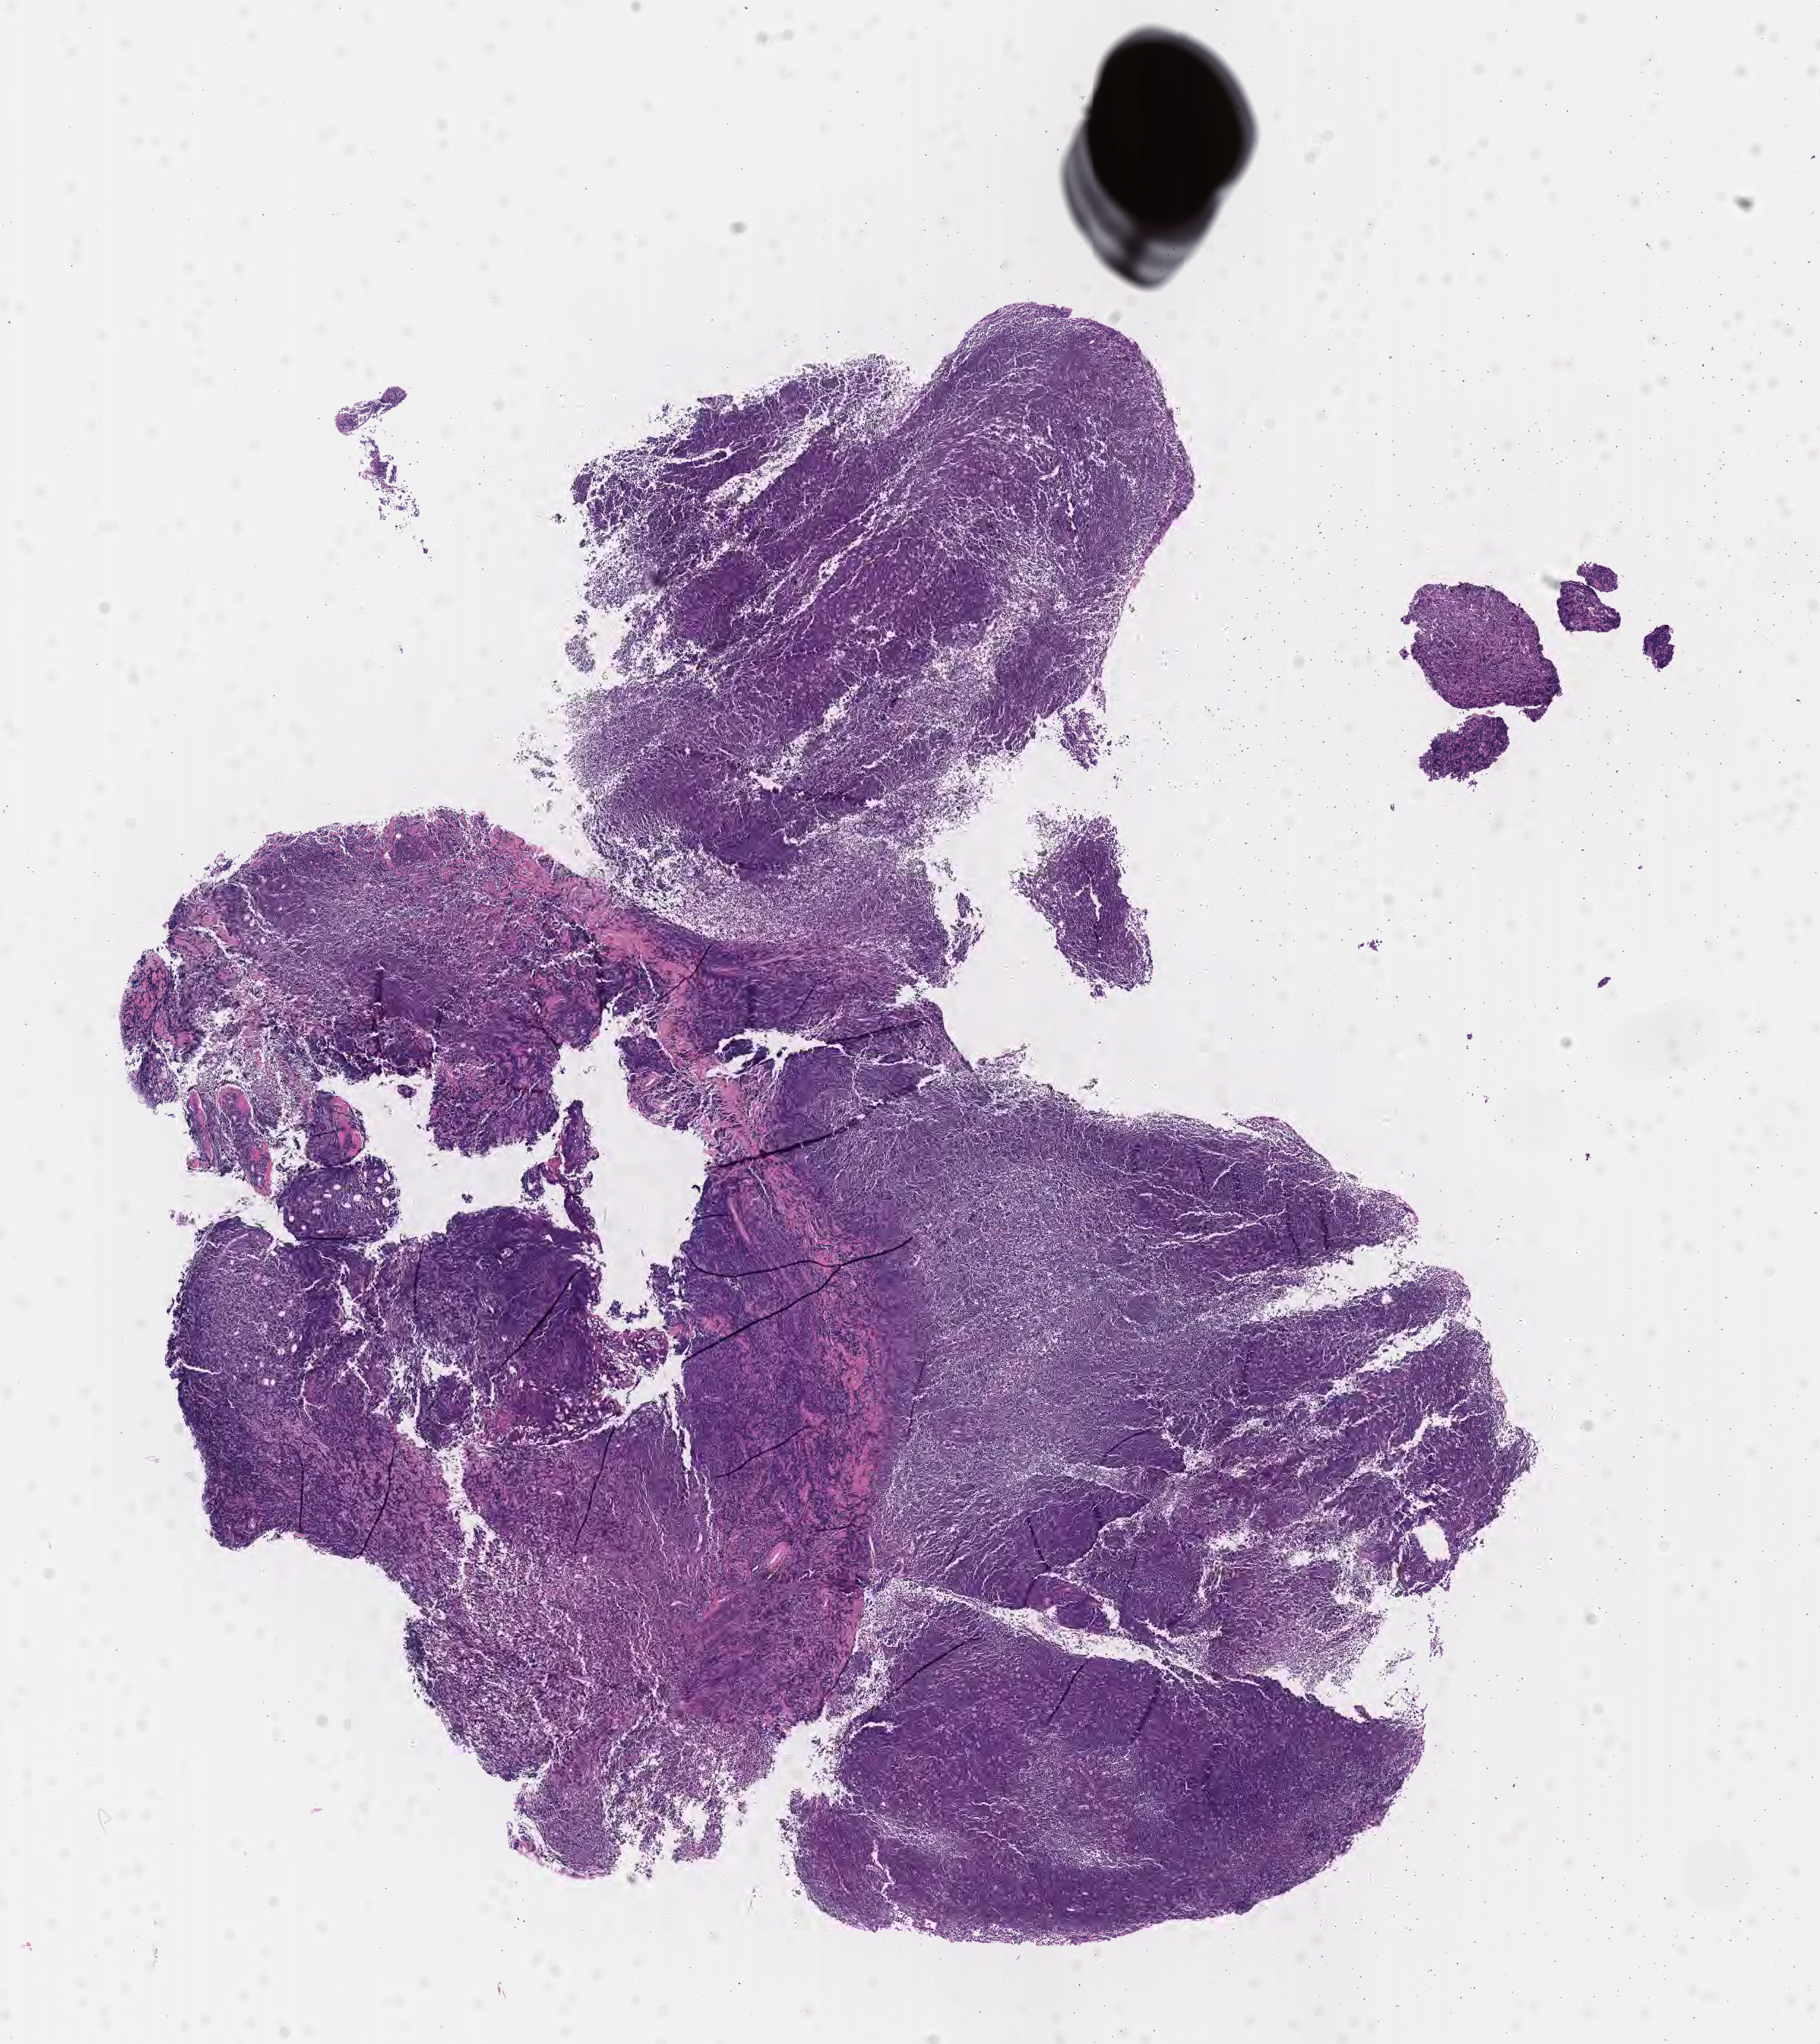
Whole-slide image, haematoxylin and eosin stain — whole scanned area (about 10.1 x 11.3 mm) shown as a low-resolution overview, tumor tissue. Male patient; age at initial diagnosis 3 years.
• diagnosis: Burkitt lymphoma, NOS